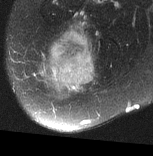
MRI of an extremity soft-tissue mass, one axial slice. T2-weighted fat-saturated. MR volume resampled by the dataset authors to the PET/CT grid (not the native acquisition matrix). 153 × 156 image matrix, field of view 149 × 152 mm. Female patient. Case-level facts recorded for this patient, not image findings: histological type: synovial sarcoma; grade: intermediate; site of the primary tumour: right buttock.
Outlined on this slice (expert contour drawn on MRI and transferred to this co-registered scan by the dataset authors):
- gross tumour volume including surrounding oedema: bounding box [x1, y1, x2, y2] px = [37, 22, 97, 96]
- gross tumour volume (mass): [42, 29, 97, 91]